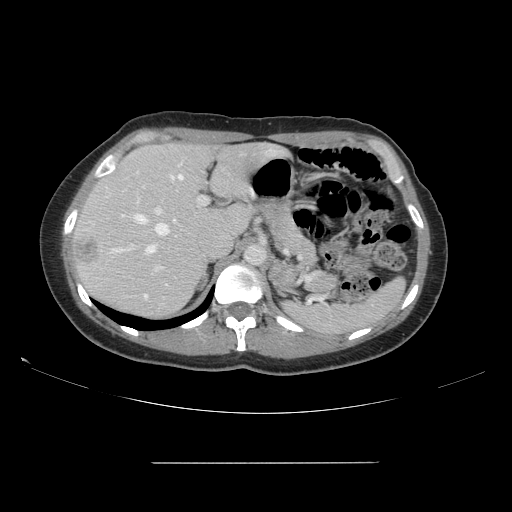
Contrast-enhanced abdominal CT, one axial slice. 120 kVp. Intravenous contrast given. Soft-tissue window (W 400 / L 40 HU). 512 × 512 image matrix, field of view 421 × 421 mm. Female patient, age 46 years. From the clinical record (not read from this slice): diagnosis: colorectal cancer liver metastases, imaged before liver resection; multiple liver metastases: yes; largest metastasis: 3 cm; chemotherapy before resection: no.
Structures marked on this image (manually delineated by an expert):
- hepatic veins: box from (x=111, y=174) to (x=183, y=254) px
- liver: (x=72, y=143)–(x=280, y=319)
- planned liver remnant (the part of the liver to remain after resection): (x=89, y=143)–(x=281, y=254)
- portal vein (with intrahepatic branches): (x=137, y=172)–(x=209, y=299)
- liver metastasis: (x=75, y=240)–(x=100, y=266)